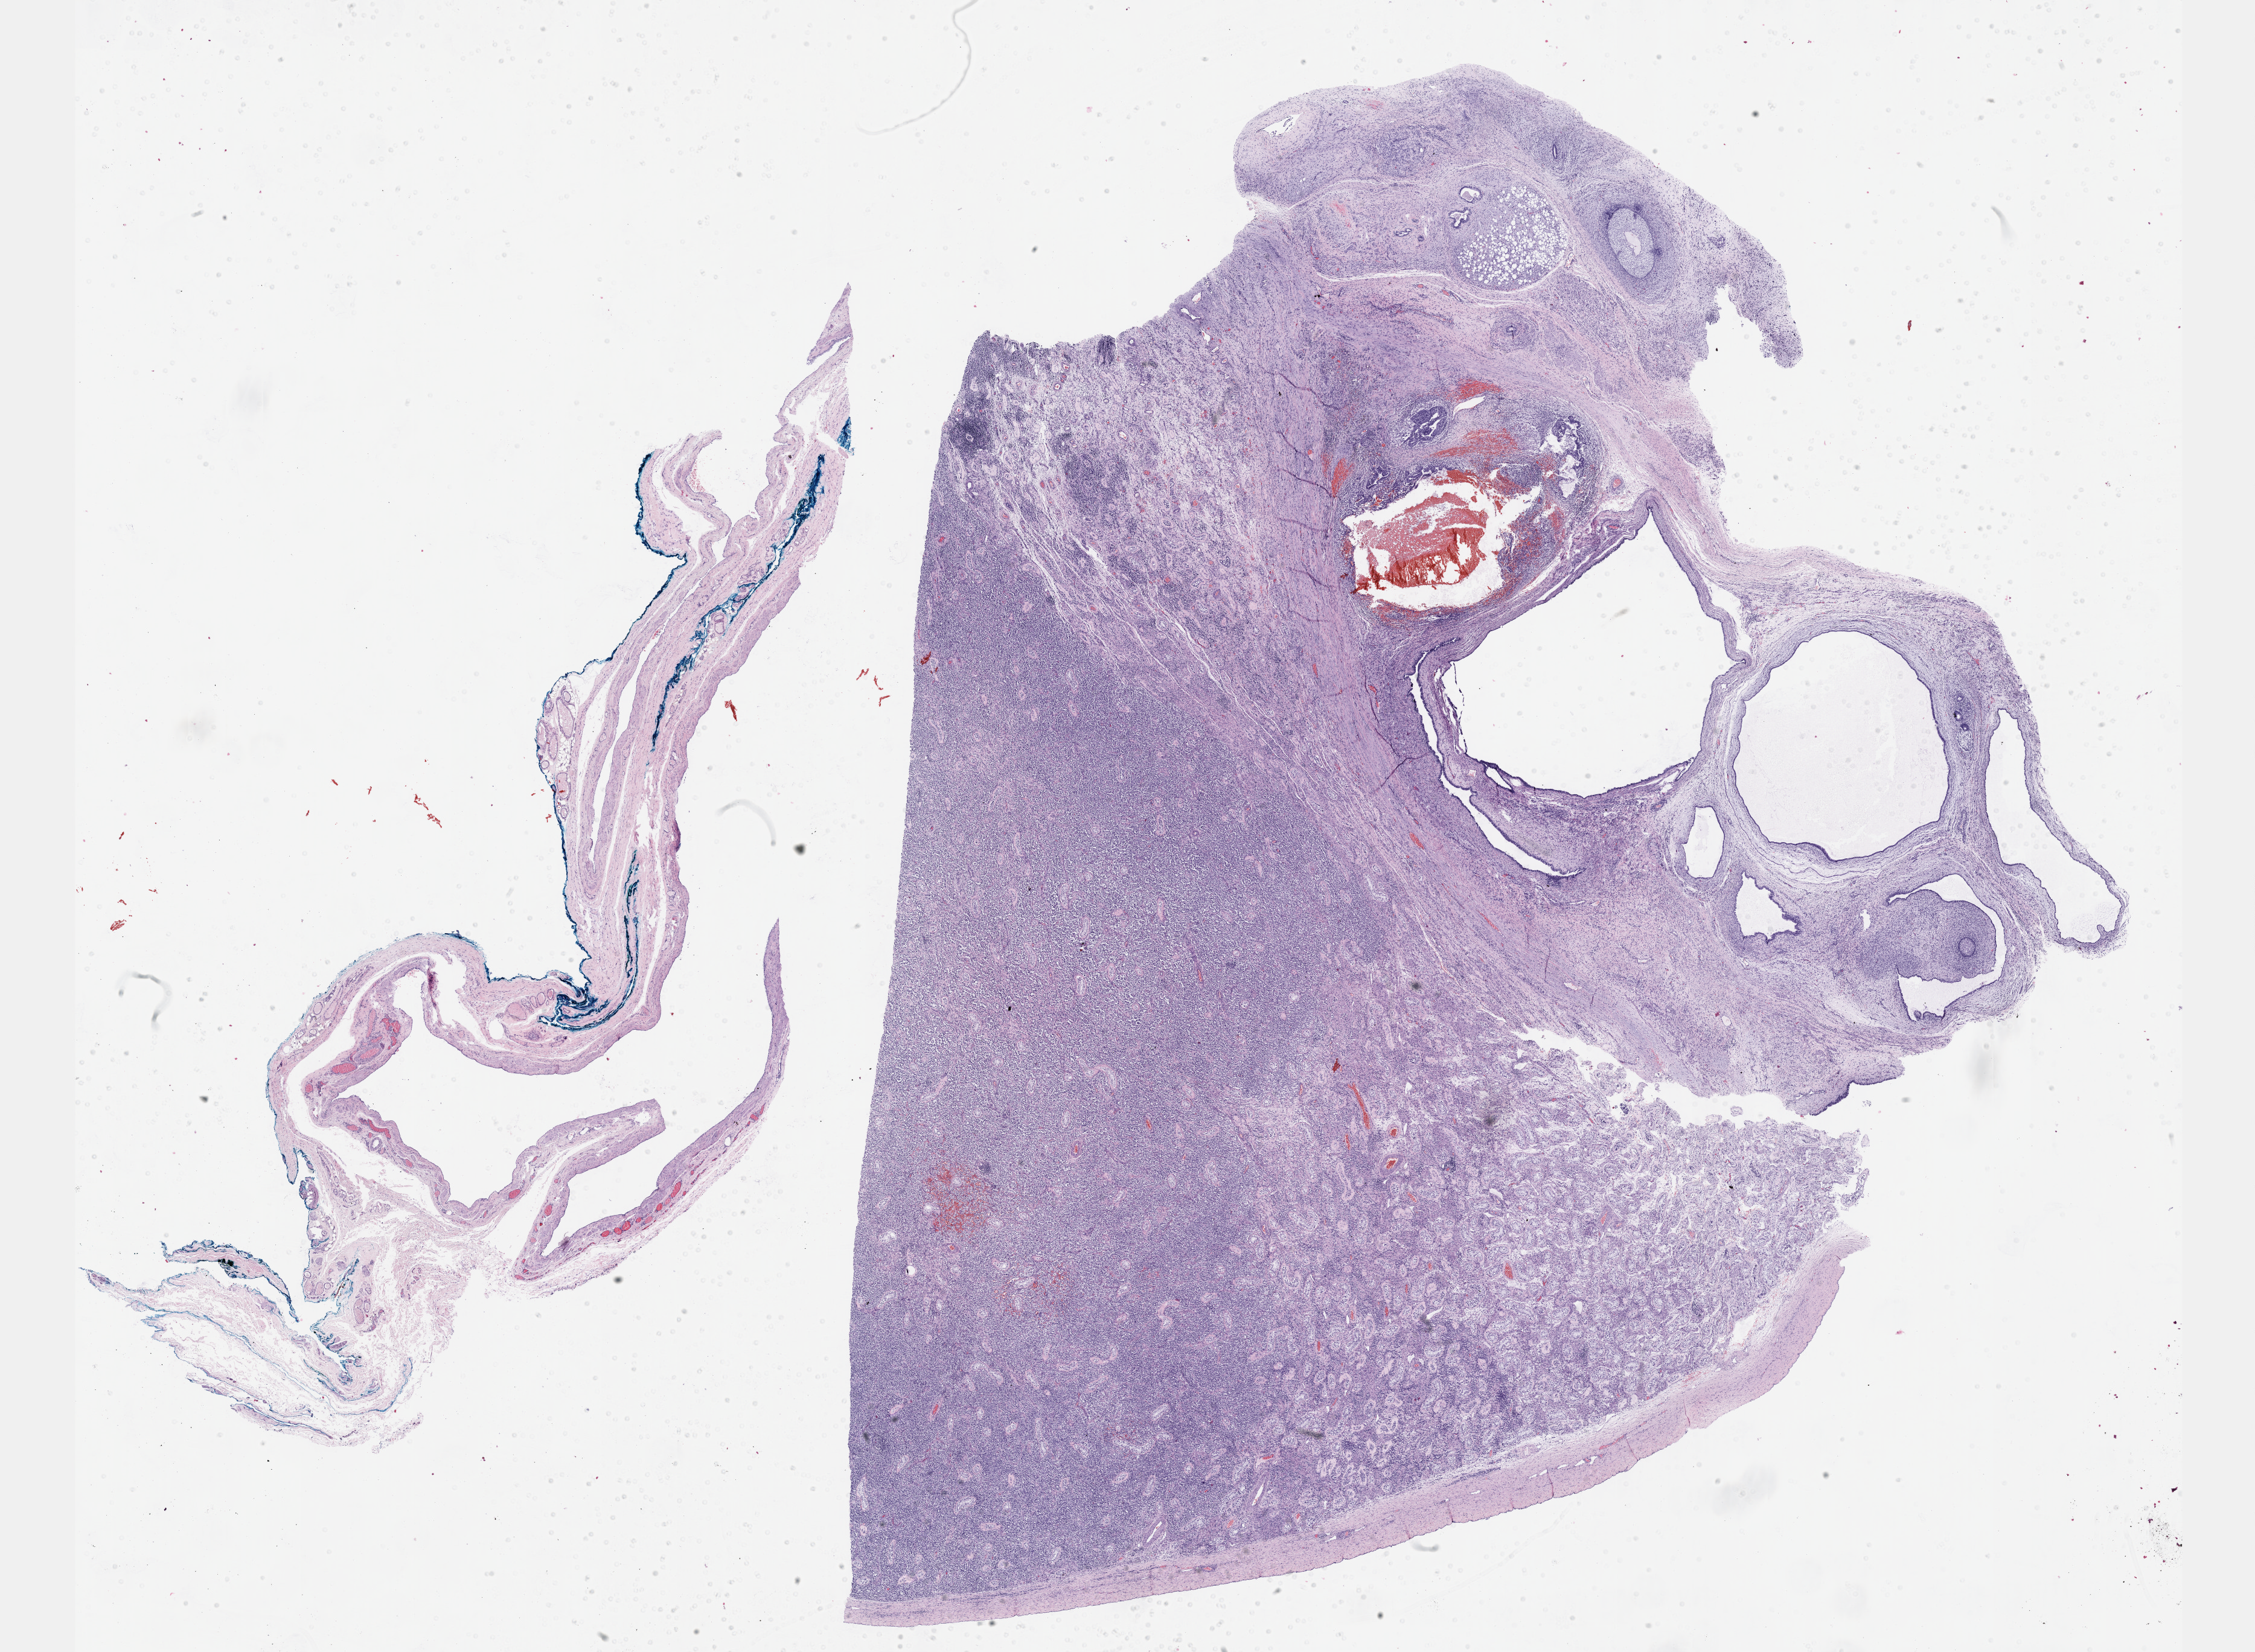
Digitized H&E-stained tissue section (whole slide) — a low-resolution overview of the entire scanned area, about 30.2 x 22.1 mm (from a 40x scan); formalin-fixed paraffin-embedded (FFPE) diagnostic section; primary tumour sample from the testis. Male, age 30 years at initial diagnosis.
Diagnosis: Mixed germ cell tumor.